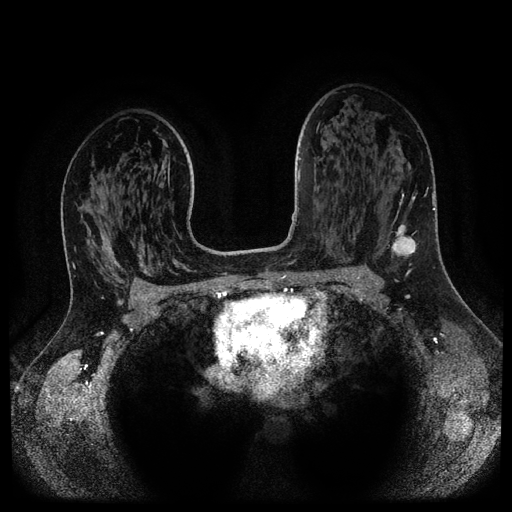
Breast MRI (dynamic contrast-enhanced, multi-phase), one axial slice. Position 67 of 116 along the scan axis. Dynamic contrast-enhanced series, time point 2 of 5 at this slice position (early post-contrast). 1.5 T. TE 2.6 ms, TR 5.3 ms. 512 × 512 image matrix, field of view 360 × 360 mm. Patient: female, 37 years.
Outlined on this slice (semi-automatic segmentation, software-assisted and operator-edited):
- breast lesion (labelled 'tumour' in the annotation; benign lesions carry a separate 'benign' label): bounding box <389,192,418,265> (left, top, right, bottom; pixels)